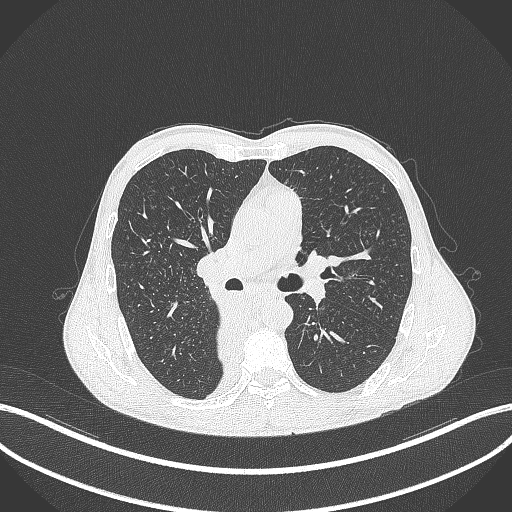
Chest CT, one axial slice; slice 223 of 371 in the series (ordered by position); lung window (W 1500 / L -600 HU); 1 mm slice thickness; 512 × 512 image matrix. Patient: male, 58 years. Case-level facts recorded for this patient, not image findings: clinical TNM (as recorded): T3 N1 M1.
Outlined on this slice (bounding box drawn by a radiologist):
- lung tumour (recorded histology: squamous cell carcinoma): bounding box [x1, y1, x2, y2] px = [215, 305, 252, 374]